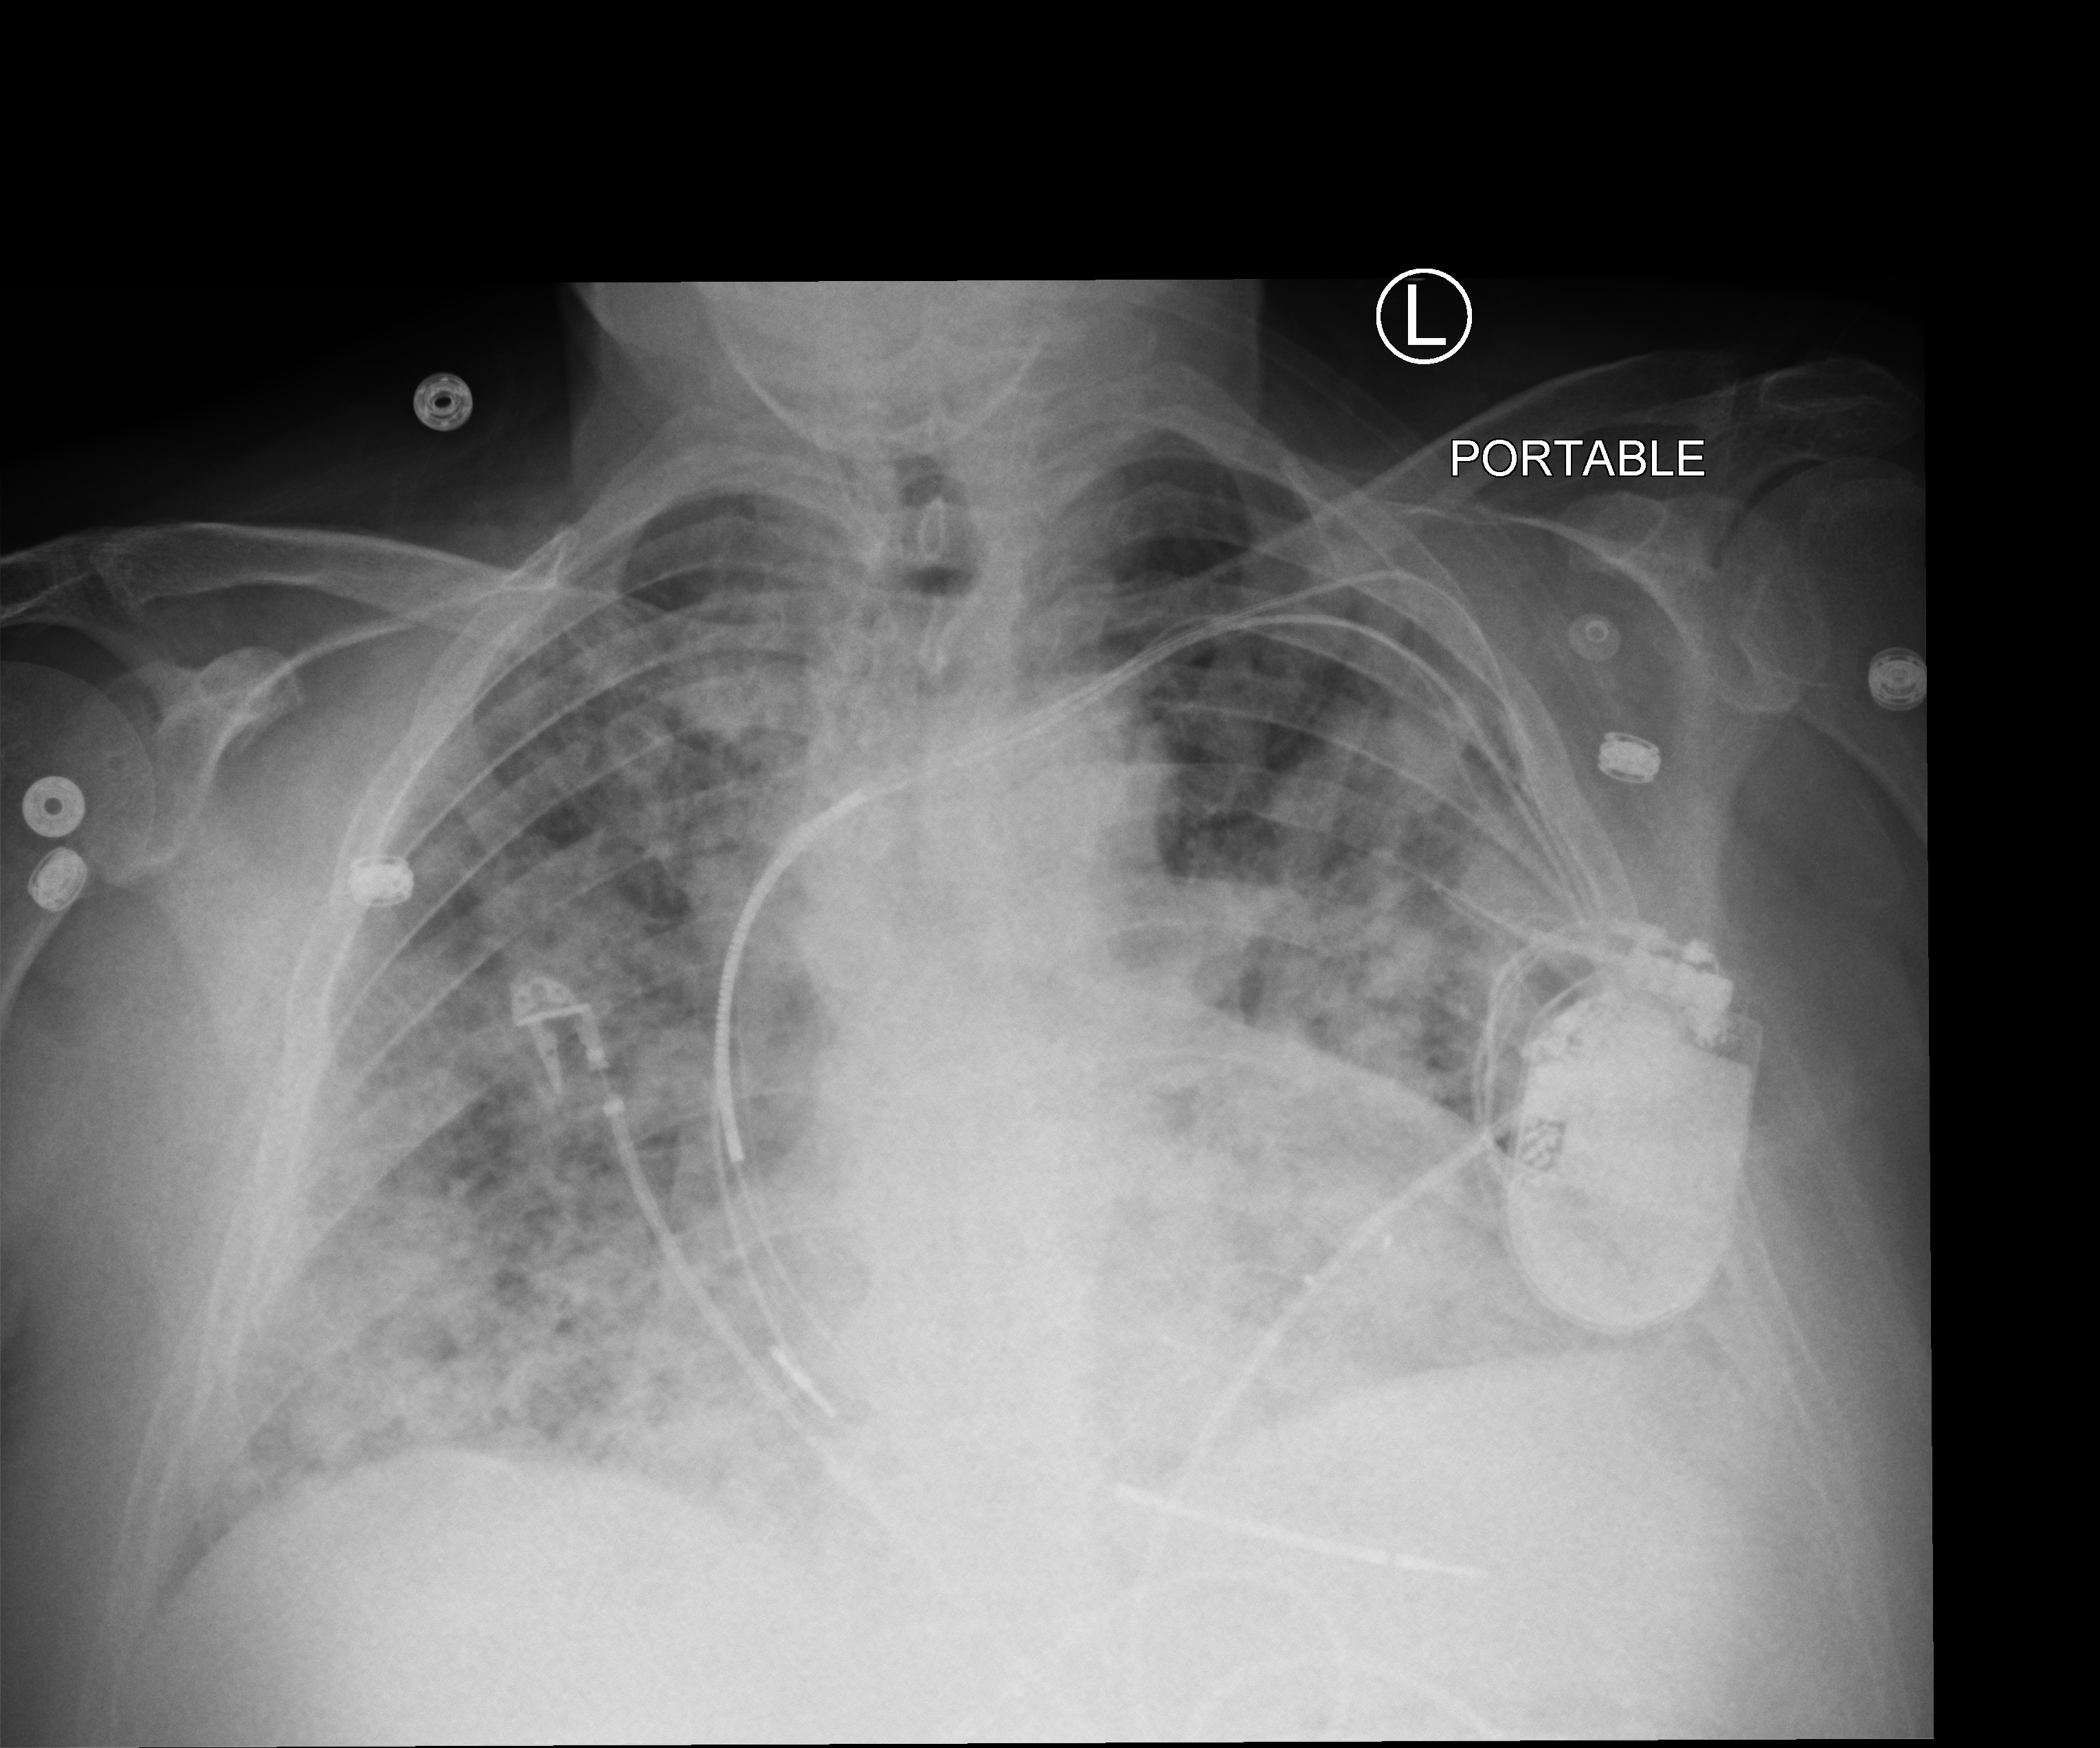
Portable chest radiograph. Male patient hospitalised with COVID-19, age 60–74 years.
From the hospital-stay record, not from the radiograph (when in the stay this image was taken is not recorded):
- mechanically ventilated during this hospital stay: no
- admitted to intensive care during this hospital stay: no